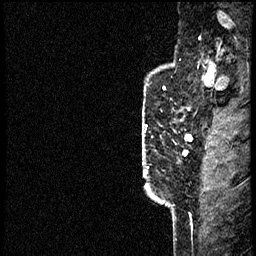
Breast MRI (dynamic contrast-enhanced), one sagittal slice; position 53 of 60 along the scan axis; dynamic contrast-enhanced study with each time point stored as its own series, time point 2 of 4 at this slice position (early post-contrast, ordered by acquisition time); 1.5 T; TE 4.2 ms, TR 17.6 ms; 2 mm slice thickness; 256 × 256 image matrix. Patient: female, 40 years. From the clinical record (not read from this slice): setting: breast cancer imaged before/during neoadjuvant chemotherapy; receptor status: HER2-positive.
Annotated regions visible in this slice (semi-automatically segmented with operator editing):
- analysis volume of interest (the breast-tissue region the enhancement analysis was run in; not a lesion): bounding box (x1, y1, x2, y2) in pixels: (142, 56, 197, 205)
- tumour enhancement mask (voxels above the 100 % enhancement threshold inside the analysis volume of interest): (142, 124, 191, 138)